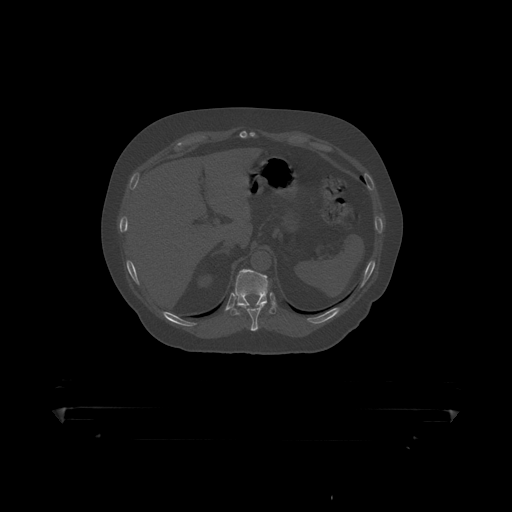
CT including the spine, one axial slice. Position 204 of 390 along the scan axis. Reconstruction kernel STANDARD. 120 kVp. Bone window (W 1800 / L 400 HU). 512 × 512 image matrix, field of view 650 × 650 mm. Patient: male, 60 years. From the clinical record (not read from this slice): primary cancer: prostate.
Annotated regions visible in this slice (semi-automatically segmented with operator editing):
- T10 vertebra: bounding box <240,303,267,319> (left, top, right, bottom; pixels)
- T11 vertebra: <227,270,277,316>